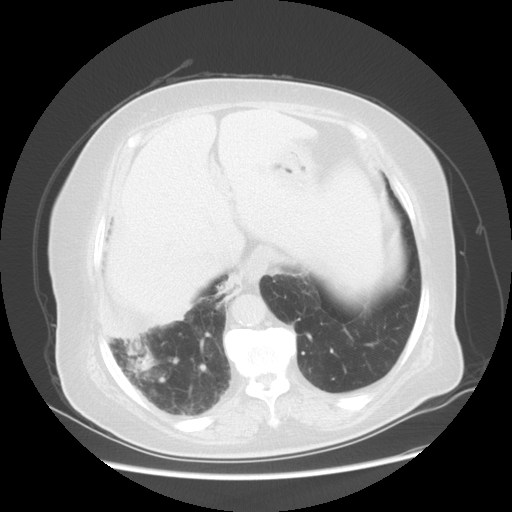
Chest CT, one axial slice; slice 12 of 56 in the series (ordered by position); reconstruction kernel STANDARD; 120 kVp; lung window (W 1500 / L -600 HU); 5 mm slice thickness; 512 × 512 image matrix, field of view 378 × 378 mm. Female patient, age 73 years. From the clinical record (not read from this slice): clinical TNM (as recorded): T3 N0 M0.
Annotated regions visible in this slice (rectangle marked by the reading radiologist):
- lung tumour (recorded histology: adenocarcinoma): box from (x=122, y=333) to (x=176, y=390) px